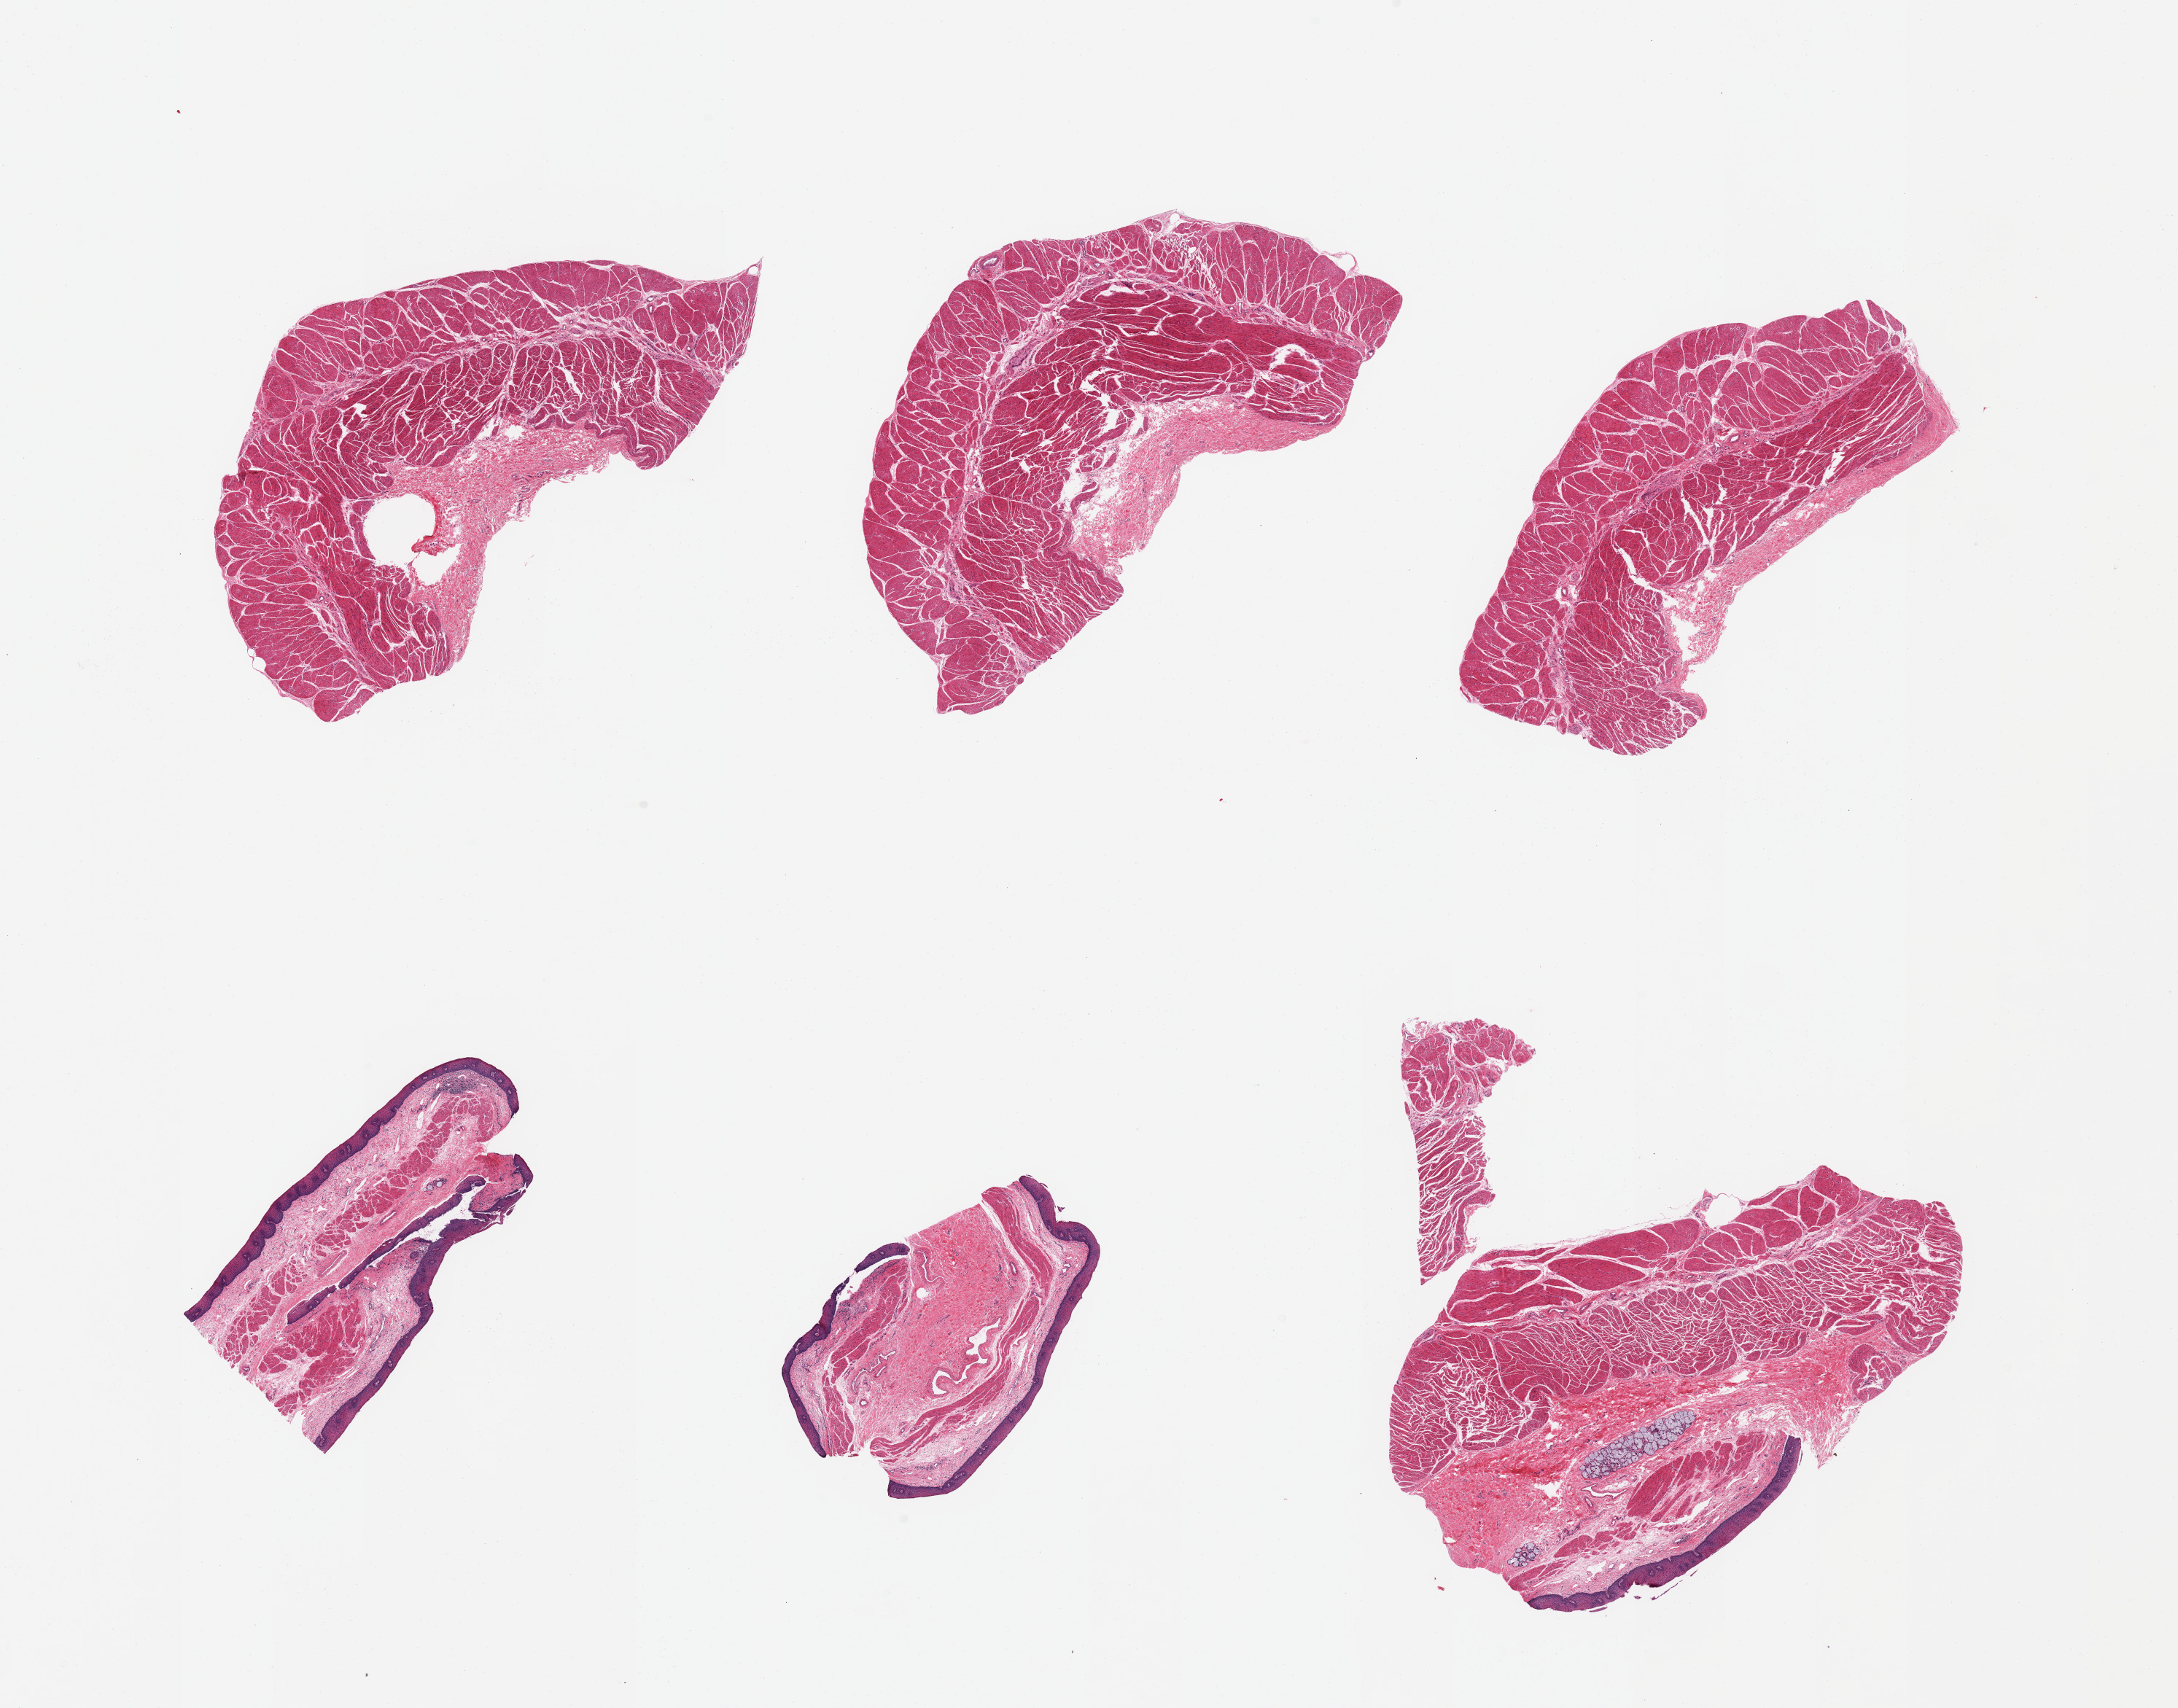
Digitized H&E-stained section — low-resolution overview of the scanned area, about 23.6 x 18.5 mm (slide scanned at 20x), PAXgene-fixed paraffin-embedded (PFPE) section, section of esophageal muscle (target tissue), tissue donor sample. Donor sex: female.
Review note (as recorded): 6 pieces; target muscularis; 3 pieces with squamous epithelium, submucosa and submucosal glands.